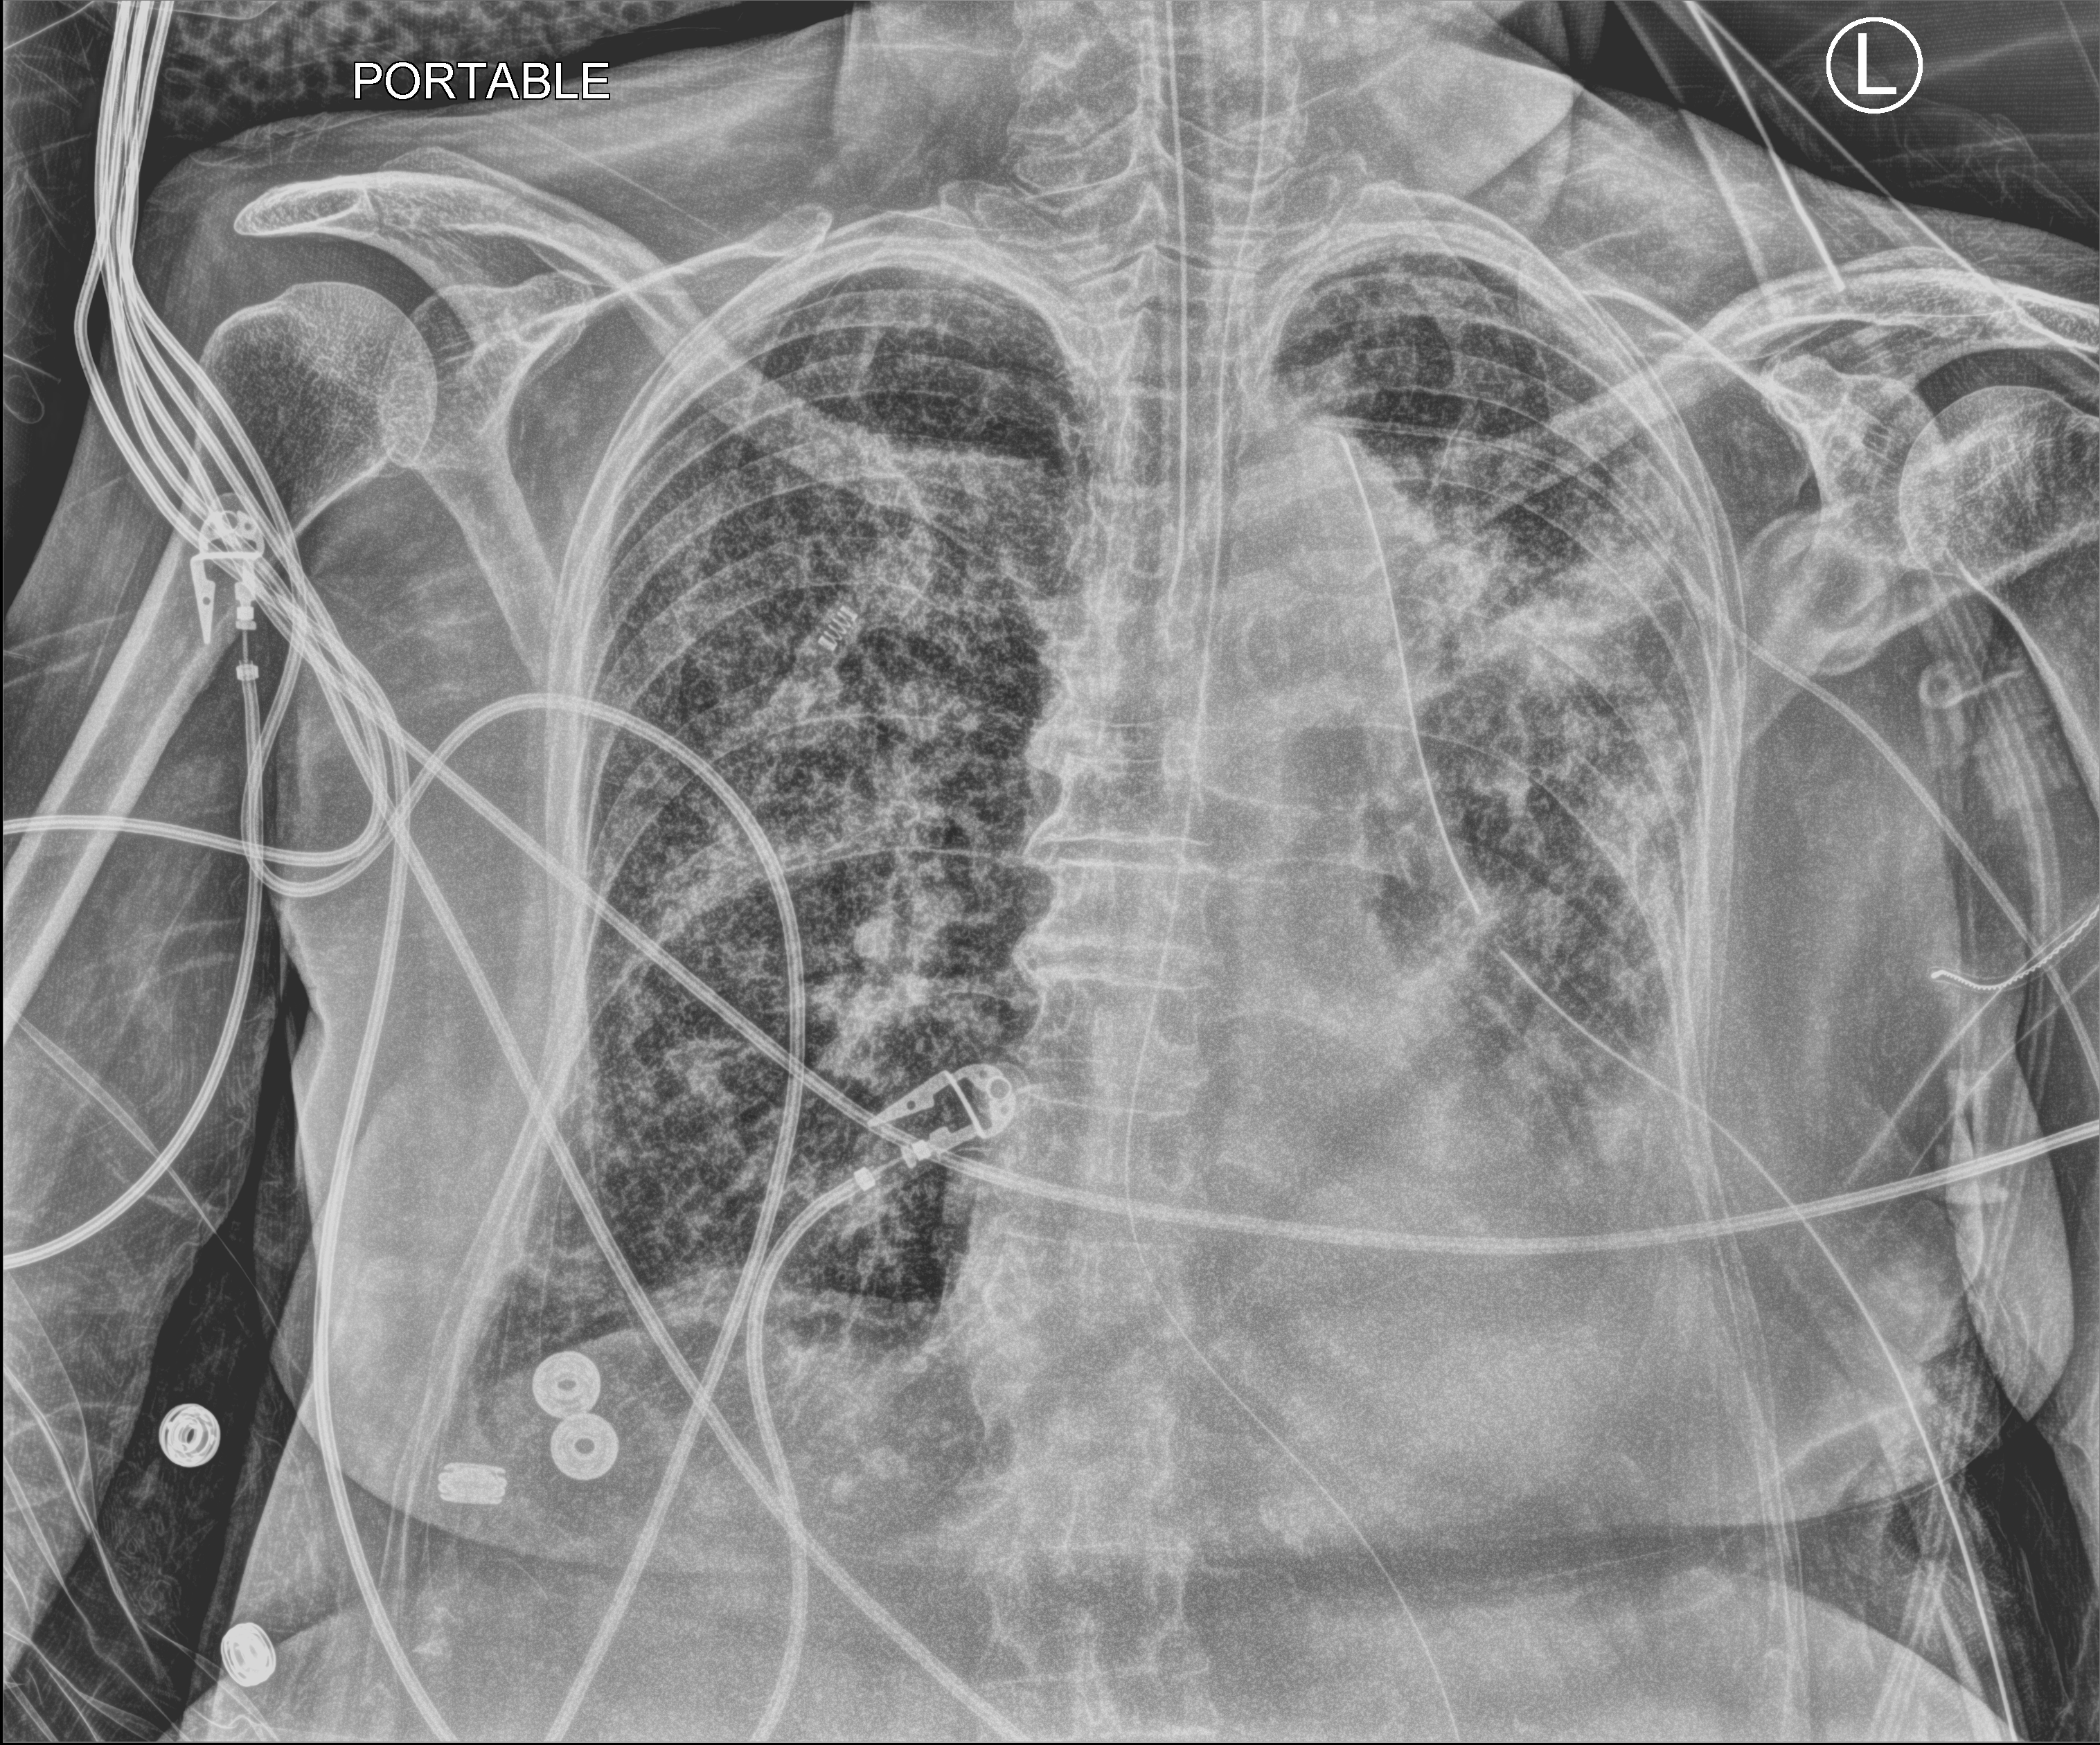
Bedside chest radiograph (computed radiography), anteroposterior (AP) projection. Patient hospitalised with COVID-19; female, aged 75–90 years.
Admission-level facts for this patient (not findings on this image; timing relative to this image not recorded): mechanically ventilated during this hospital stay: yes.